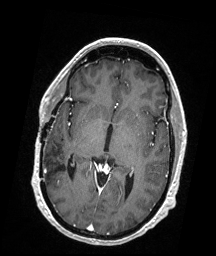
Brain MRI from a brain-tumour surgery series, one axial slice; position 97 of 176 along the scan axis; T1-weighted post-contrast; 1 mm slice thickness; 216 × 256 image matrix, field of view 211 × 250 mm. From the clinical record (not read from this slice): histopathology: Demyelinating Lesions (Multiple Sclerosis Plaques).
Structures marked on this image (outlined manually by an expert reader):
- tumour: bounding box [x1, y1, x2, y2] px = [121, 208, 127, 213]